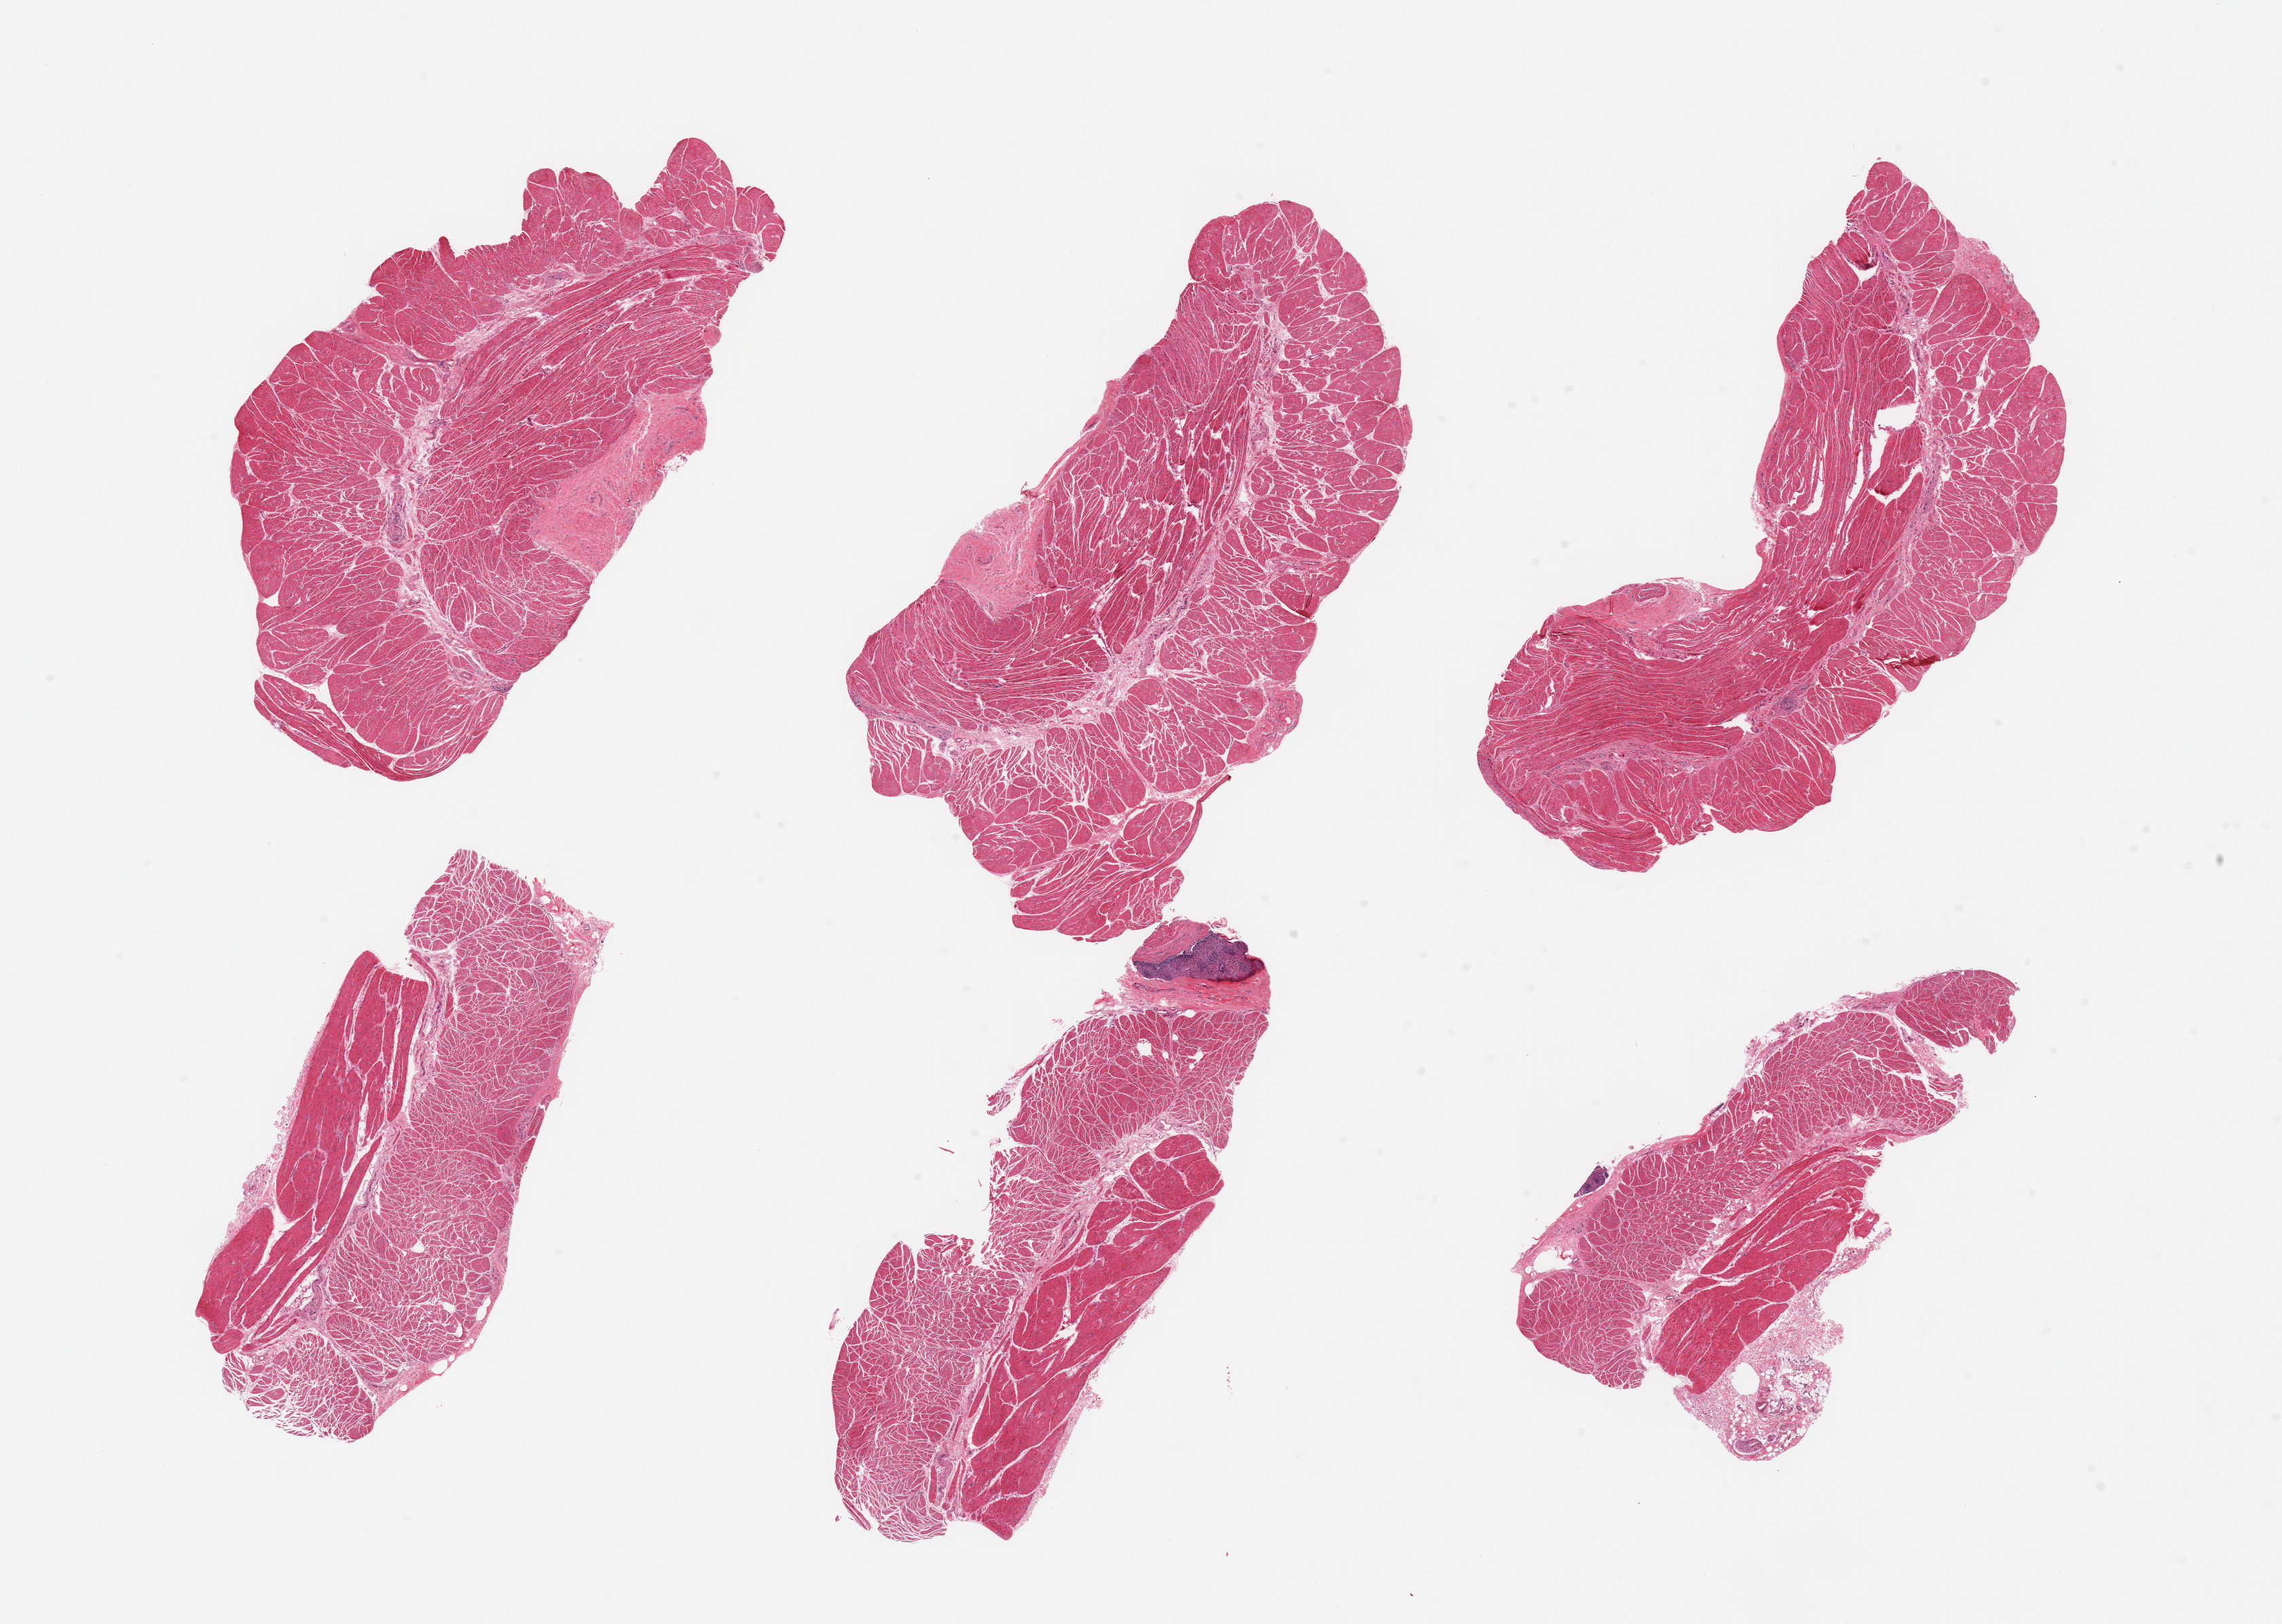
Whole-slide image, hematoxylin and eosin (H&E) stain, shown as a low-resolution overview of the whole scanned area (about 26.6 x 18.9 mm), PAXgene-fixed, paraffin-embedded tissue, target tissue: esophageal muscle, tissue donor sample. Male donor.
Reviewer comment on this tissue sample: 6 pieces; well dissected except for 2 small squamous remnants up to 1 mm.